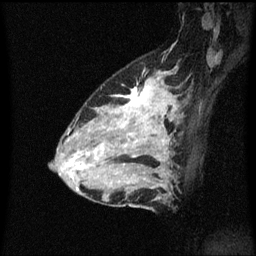
Breast MRI (dynamic contrast-enhanced), one sagittal slice; position 40 of 60 along the scan axis; dynamic contrast-enhanced series, image 2 of 3 at this slice position (ordered by acquisition); 1.5 T; TE 4.2 ms, TR 8.4 ms; 2 mm slice thickness; 256 × 256 image matrix. Female patient, age 34 years. Case-level facts recorded for this patient, not image findings: setting: breast cancer imaged before/during neoadjuvant chemotherapy; receptor status: HR-positive, HER2-negative.
Outlined on this slice (semi-automatically segmented with operator editing):
- analysis volume of interest (the breast-tissue region the enhancement analysis was run in; not a lesion): bounding box [x1, y1, x2, y2] px = [69, 70, 177, 209]
- tumour enhancement mask (voxels above the 70 % enhancement threshold inside the analysis volume of interest): [70, 80, 174, 189]